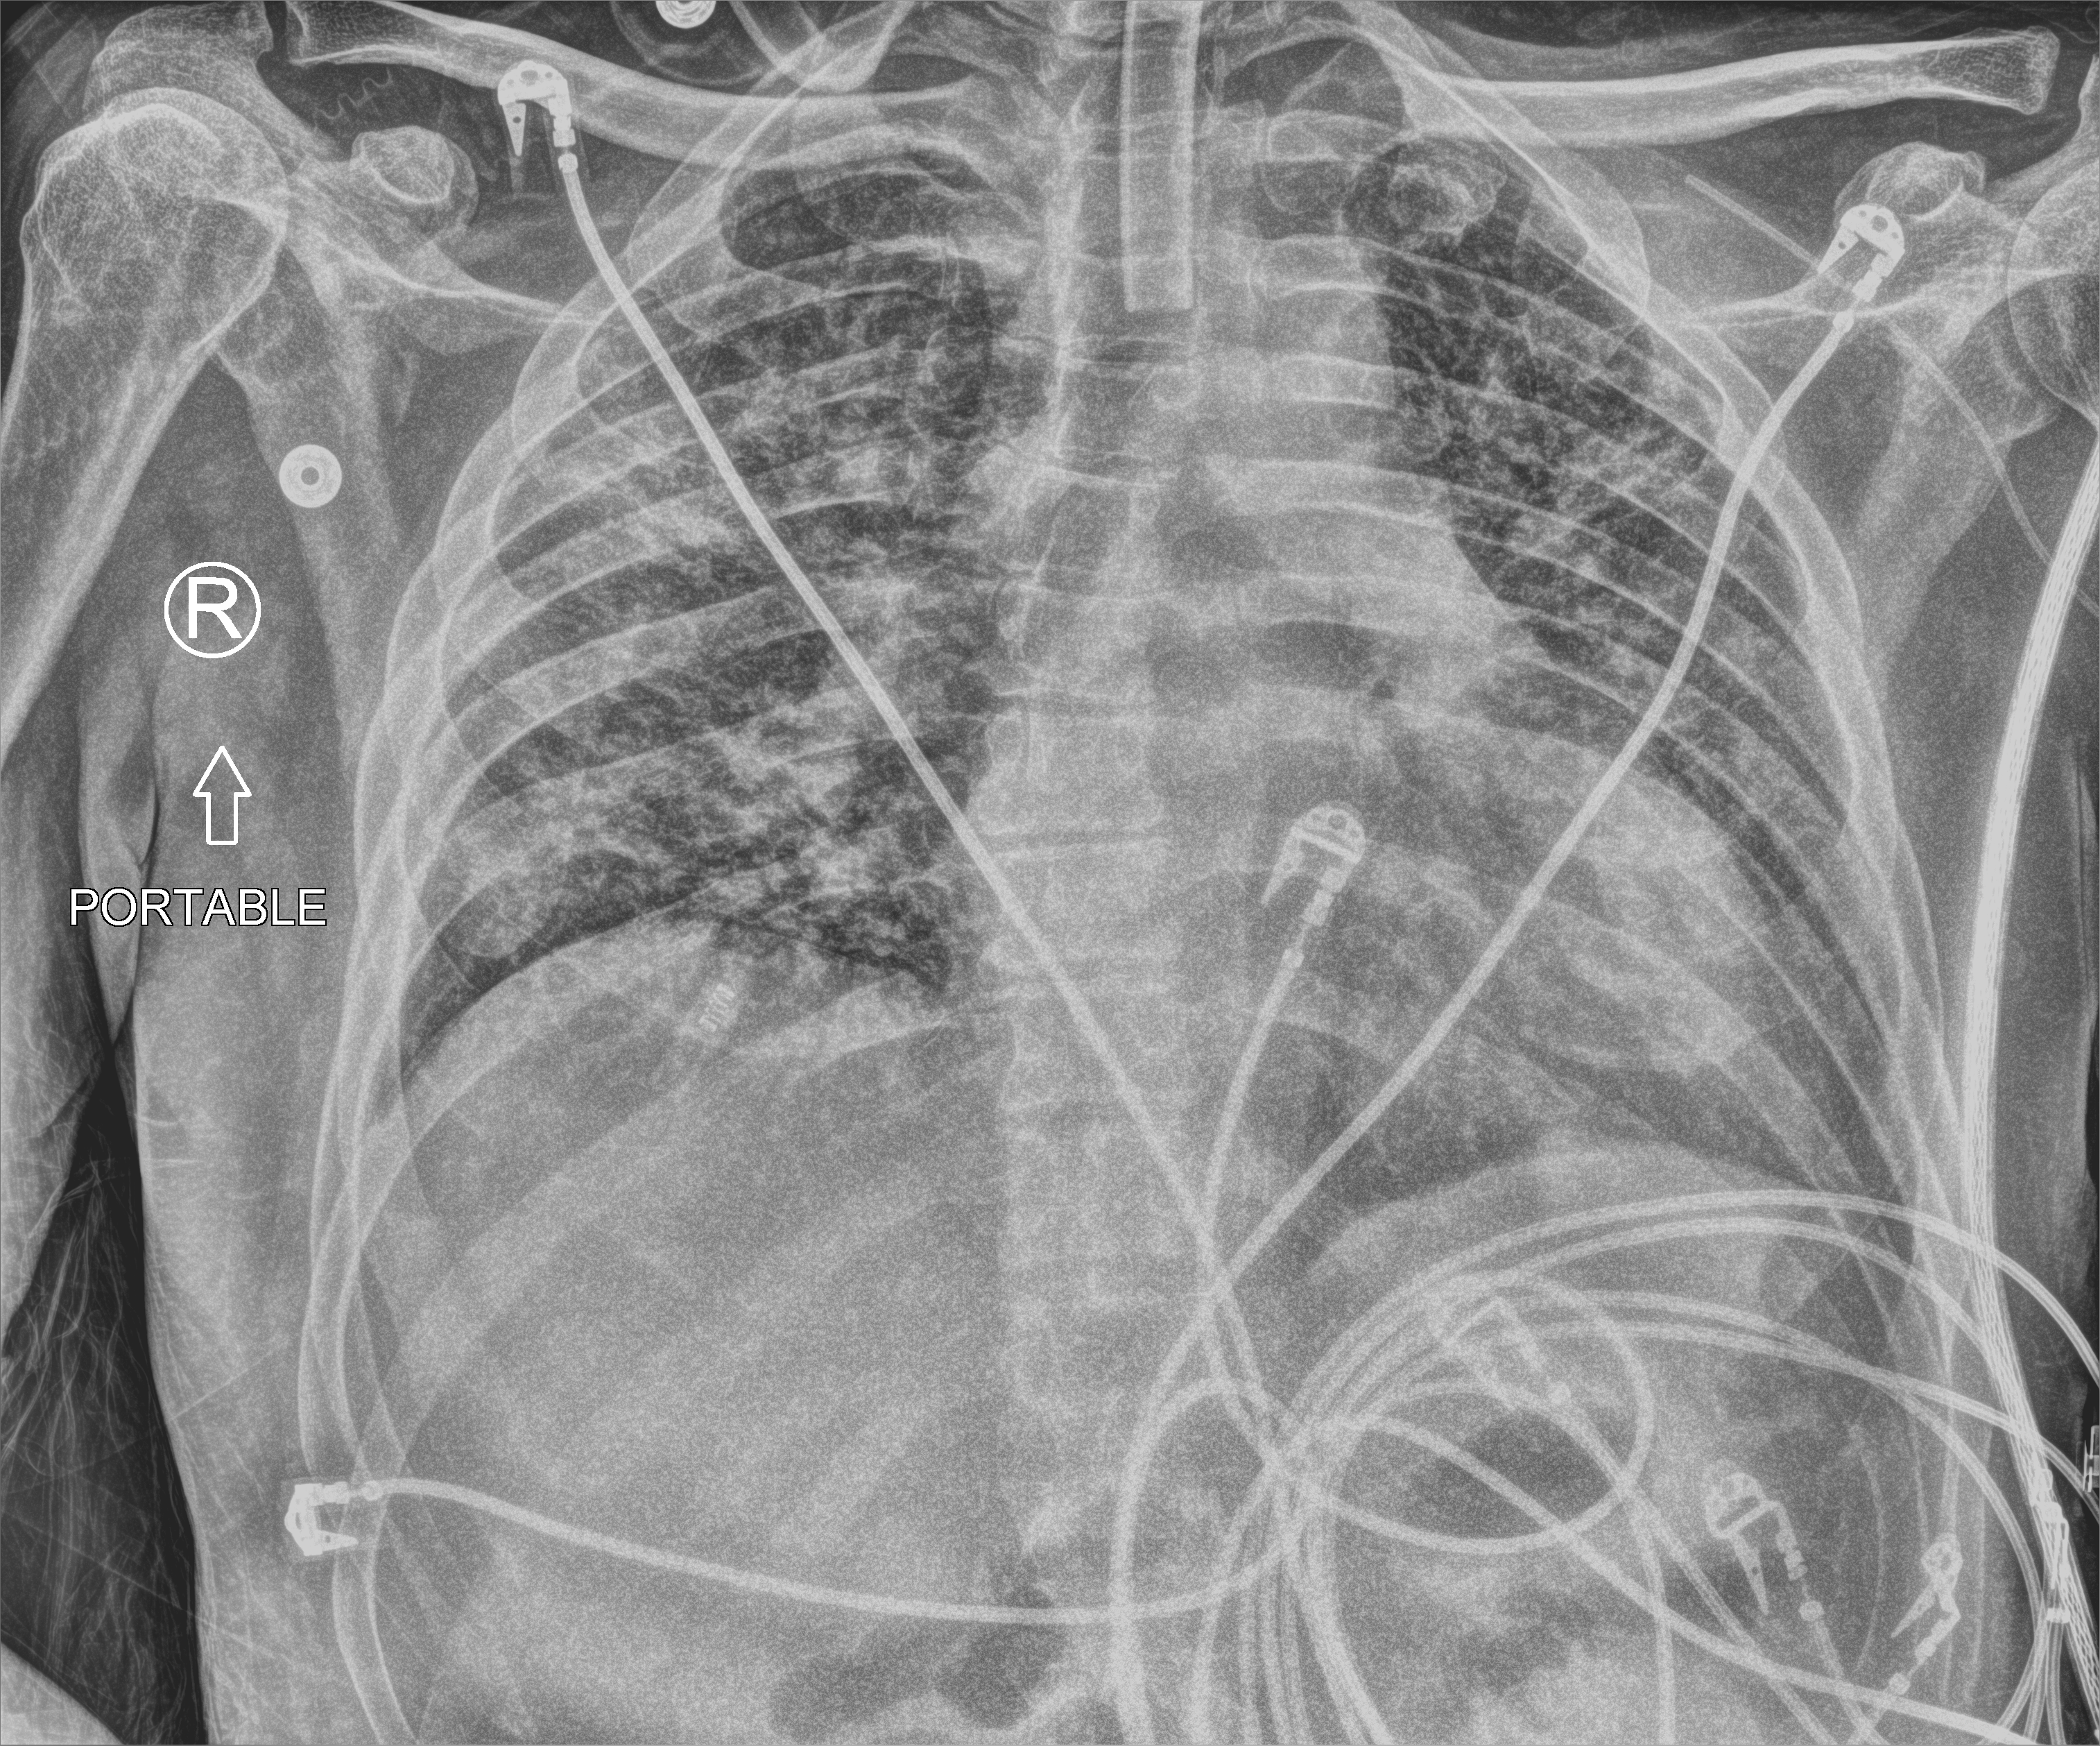
Chest X-ray (portable). Male patient hospitalised with COVID-19, age 18–59 years.
Hospital-stay facts (about this admission, not read from this image; timing relative to this image not recorded): admitted to intensive care during this hospital stay: yes; mechanically ventilated during this hospital stay: yes.